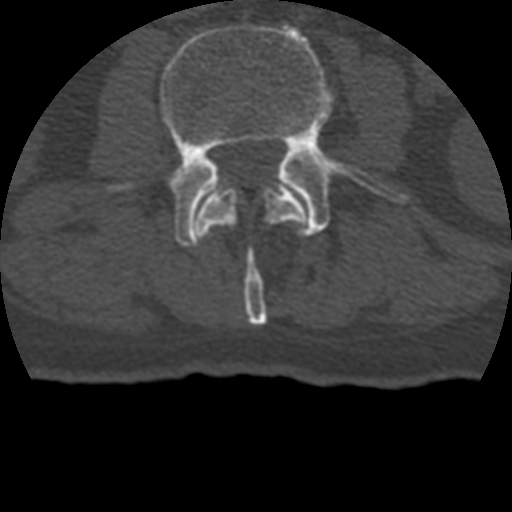
CT including the spine, one axial slice. Position 99 of 399 along the scan axis. Reconstruction kernel STANDARD. Bone window (W 1800 / L 400 HU). 512 × 512 image matrix. Patient age 69 years. Case-level facts recorded for this patient, not image findings: primary cancer: prostate.
Annotated regions visible in this slice (semi-automatically segmented with operator editing):
- L2 vertebra: box from (x=196, y=187) to (x=307, y=326) px
- L3 vertebra: (x=160, y=24)–(x=408, y=246)